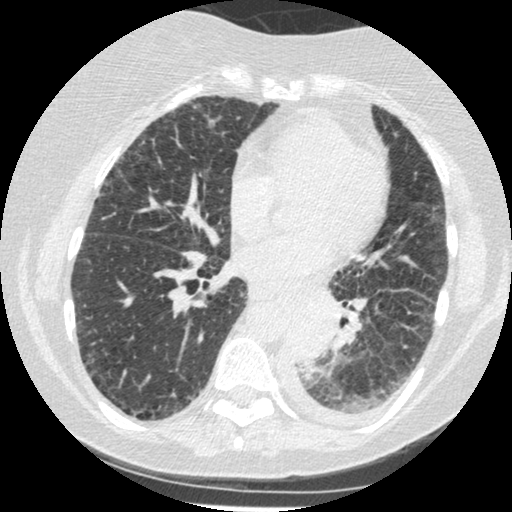
Low-dose screening chest CT, axial slice; third screening round (two years after baseline); lung window (W 1500 / L -600 HU); standard (soft-tissue) reconstruction kernel (STANDARD); slice 243 of 341 in the series. Female participant, aged 60 years at enrolment.
Expert-annotated lung lesion, bounding box <277,303,344,376> (left, top, right, bottom; pixels). Reader record for this screening exam (exam-level; its link to the box is not recorded): non-calcified nodule or mass ≥4 mm, left lower lobe, 54 × 38 mm, smooth margins, soft tissue attenuation, pre-existing on the prior screen: yes; interval growth: yes. Participant outcome: lung cancer diagnosed 15 days after this screen — small cell carcinoma, NOS, left lower lobe, undifferentiated (G4), stage IV (AJCC 6th edition), 69 mm at pathology.